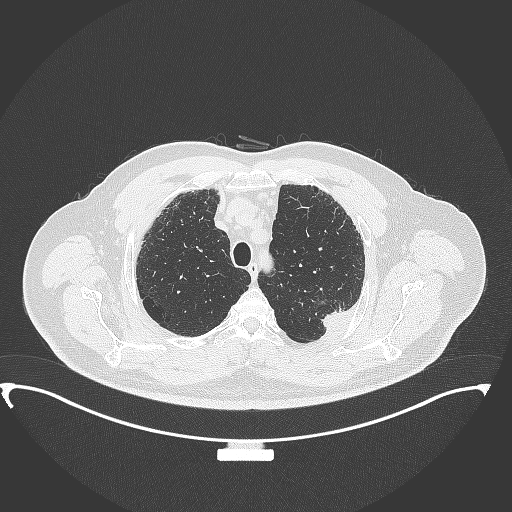
Chest CT, one axial slice; position 293 of 350 along the scan axis; 120 kVp; lung window (W 1500 / L -600 HU); 512 × 512 image matrix, field of view 459 × 459 mm. Patient: male, 64 years. Case-level facts recorded for this patient, not image findings: clinical TNM (as recorded): T1c N1 M1.
Outlined on this slice (rectangle marked by the reading radiologist):
- lung tumour (recorded histology: adenocarcinoma): bounding box (x1, y1, x2, y2) in pixels: (313, 300, 350, 331)